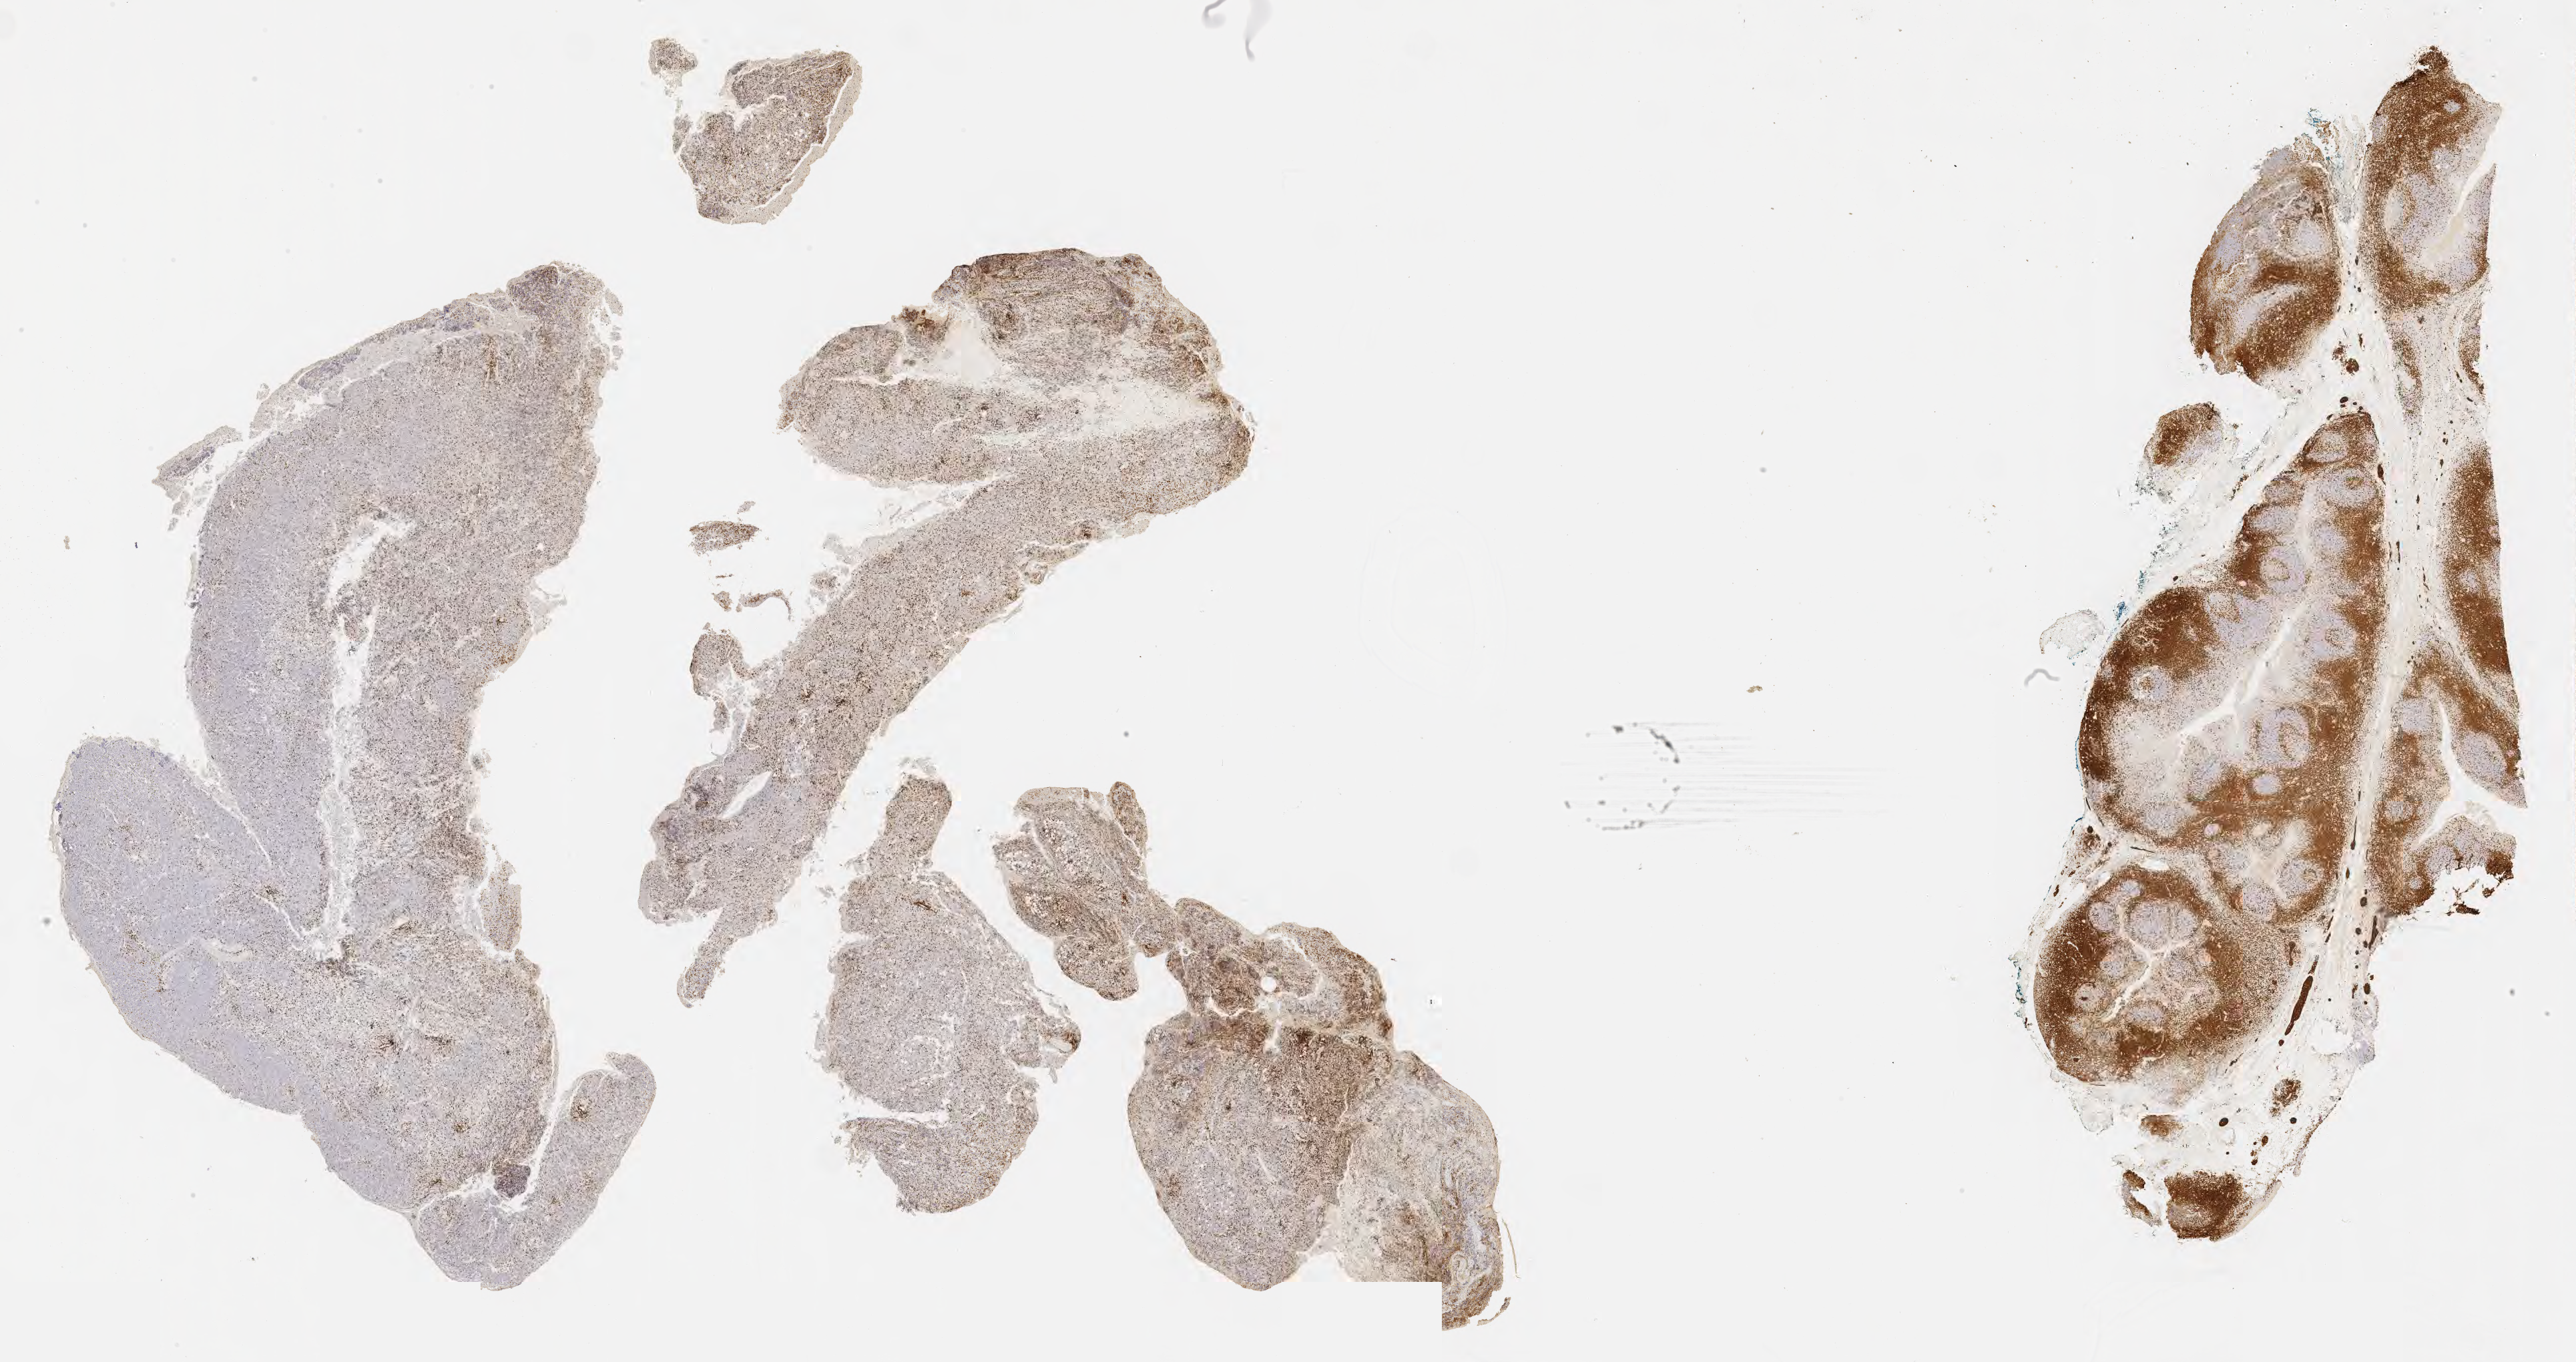
Immunohistochemistry (IHC) whole-slide image stained for CD3, shown as a low-resolution overview of the whole scanned area (about 31.2 x 16.5 mm), specimen: tumor tissue, anatomic site: abdomen proper. Patient: male, age at initial diagnosis 5 years.
Histologic diagnosis: Burkitt lymphoma, NOS.